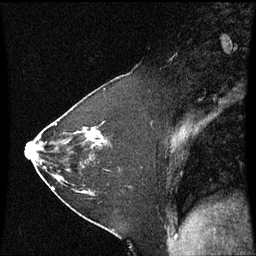
Breast MRI (dynamic contrast-enhanced), one sagittal slice. Dynamic contrast-enhanced series, image 2 of 3 at this slice position (ordered by acquisition). 1.5 T. TE 4.2 ms, TR 8.9 ms. 2 mm slice thickness. 256 × 256 image matrix. Patient: female, 37 years. From the clinical record (not read from this slice): setting: breast cancer imaged before/during neoadjuvant chemotherapy; receptor status: HR-positive, HER2-negative.
Outlined on this slice (semi-automatic segmentation, software-assisted and operator-edited):
- analysis volume of interest (the breast-tissue region the enhancement analysis was run in; not a lesion): bounding box [x1, y1, x2, y2] px = [60, 102, 122, 181]
- tumour enhancement mask (voxels above the 70 % enhancement threshold inside the analysis volume of interest): [103, 136, 108, 145]